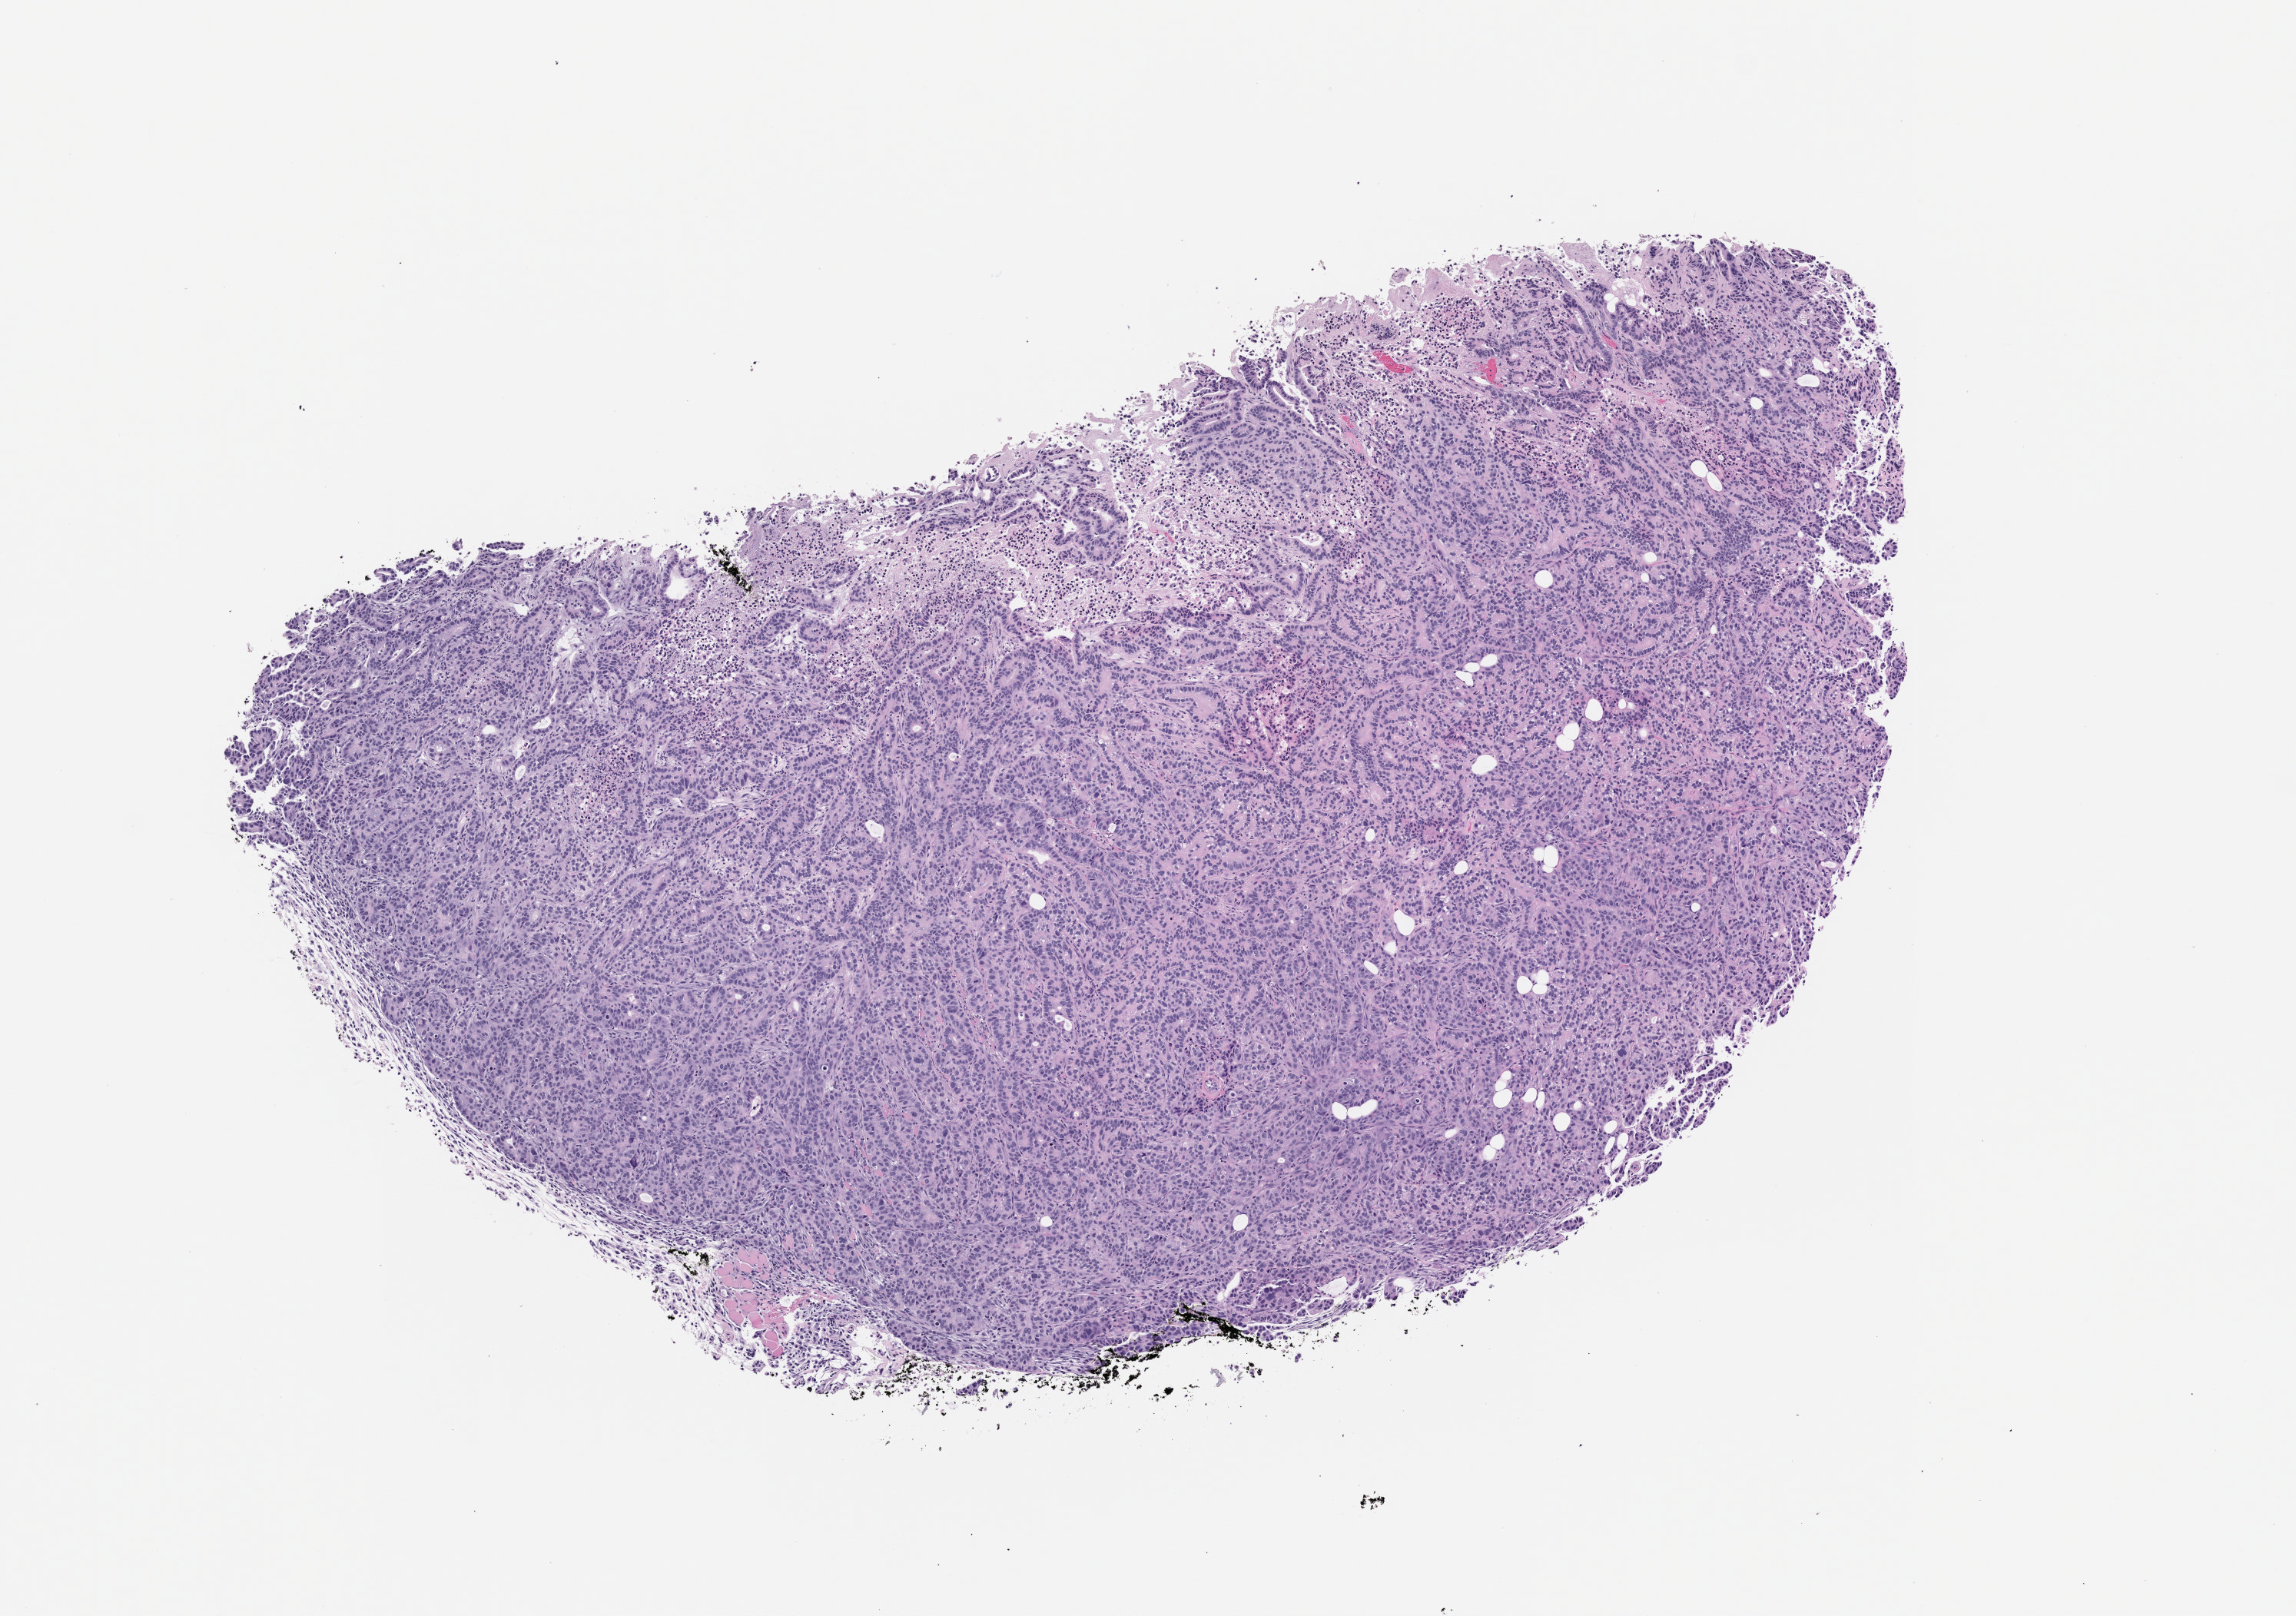
Whole-slide image, hematoxylin and eosin (H&E): patient-derived xenograft (human tumor grown in a mouse), passage 2 — low-resolution overview of the scanned area, about 6.0 x 4.2 mm. Formalin-fixed paraffin-embedded section. Tumor site category: pancreas.
Originating patient diagnosis: Pancreatic Adenocarcinoma.